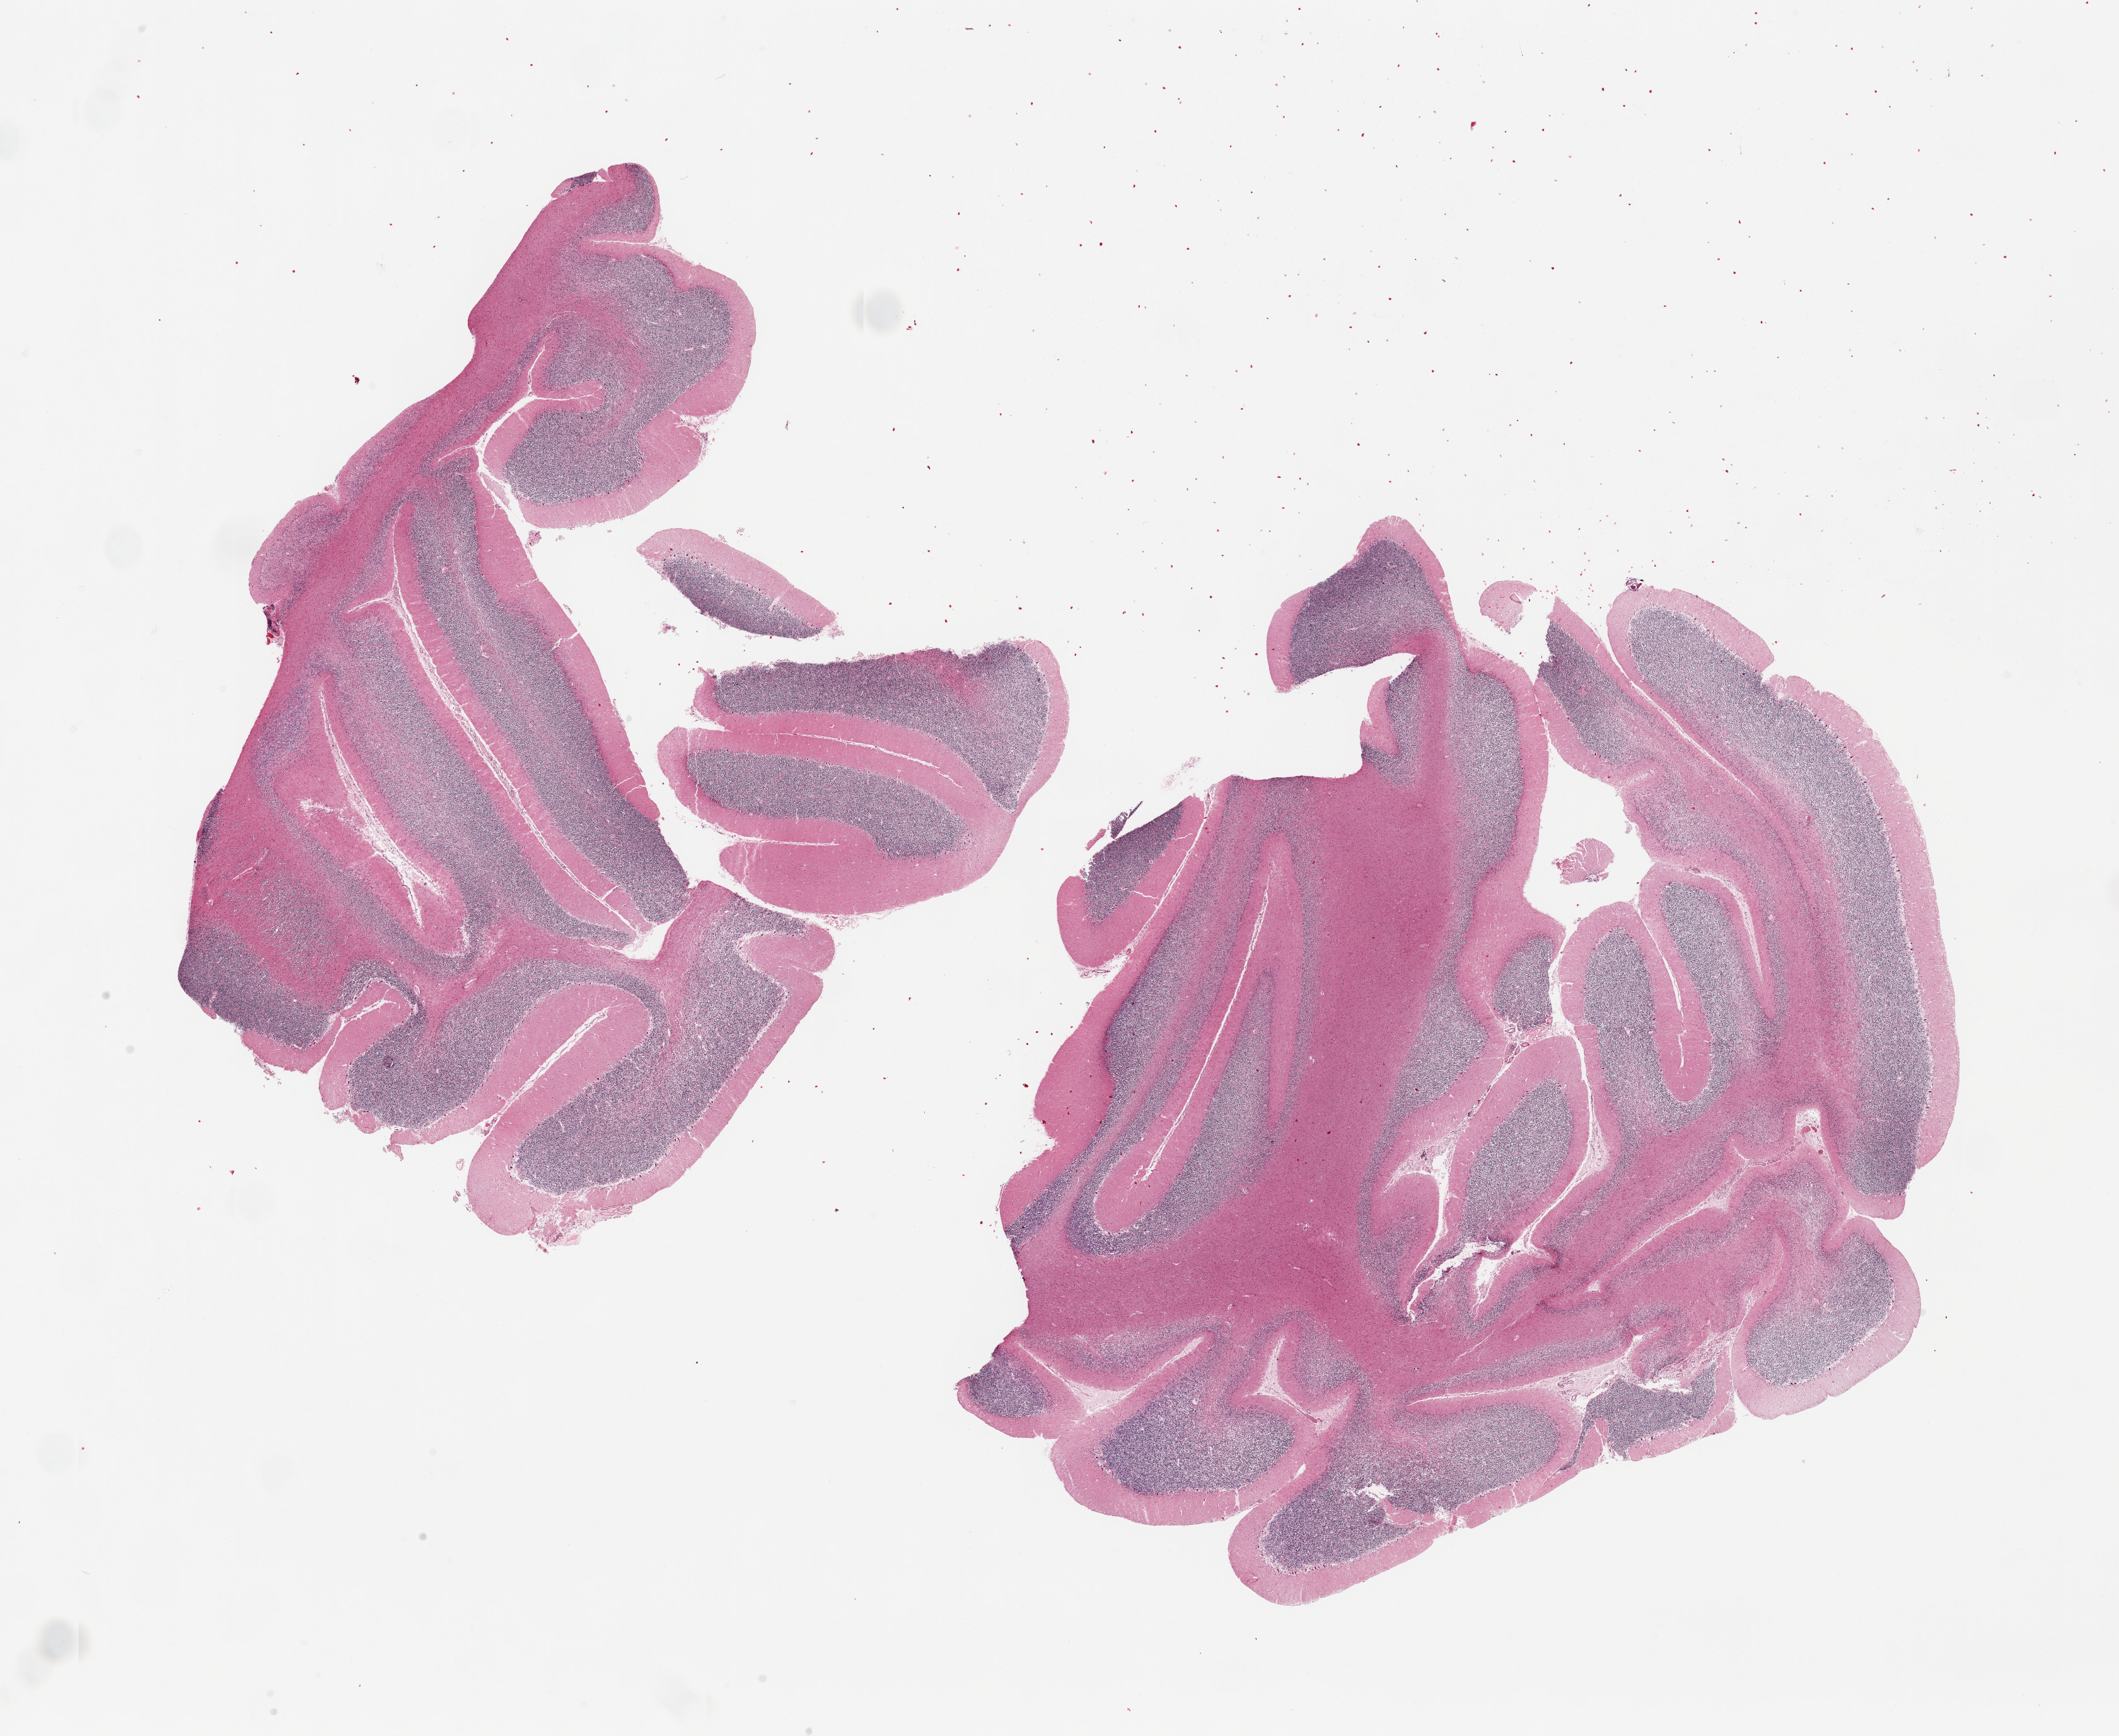
Hematoxylin and eosin (H&E) whole-slide image, low-resolution overview of the scanned area, about 26.6 x 21.8 mm (slide scanned at 20x); PAXgene-fixed paraffin-embedded (PFPE) section; sampled site (target tissue): cerebellum; tissue donor sample.
Pathologist's review note for this sample: 2 pieces, cardiac atrium, no abnormalities.